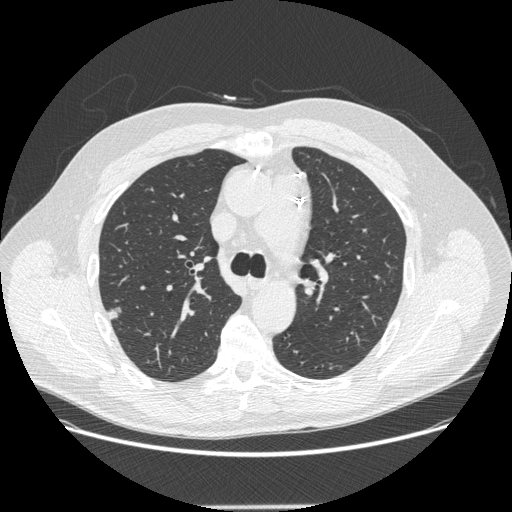
Low-dose screening chest CT, one axial slice; slice 190 of 265 in the series (ordered by position); reconstruction kernel STANDARD; 120 kVp; lung window (W 1500 / L -600 HU); 512 × 512 image matrix.
Structures marked on this image (expert manual segmentation):
- lesion 1 (tumor, upper lobe of right lung): bounding box [x1, y1, x2, y2] px = [109, 307, 122, 319]